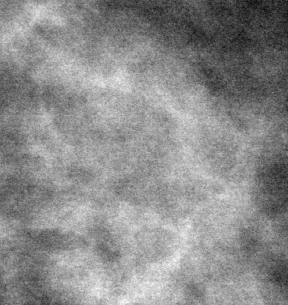
Crop from a digitized film mammogram around one marked abnormality; left breast; CC view; BI-RADS breast density category 1 (scale 1–4).
Marked abnormality: mass, shape oval, margins microlobulated; BI-RADS assessment category 4; subtlety rating 4 on a 1 (subtle) to 5 (obvious) scale; pathology result (as recorded, not read from the image): malignant.